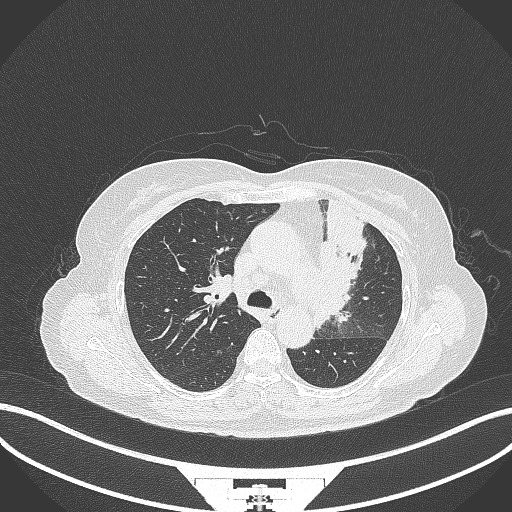
Chest CT, one axial slice; position 224 of 382 along the scan axis; lung window (W 1500 / L -600 HU); 512 × 512 image matrix. Patient: female, 64 years. From the clinical record (not read from this slice): clinical TNM (as recorded): T2a N2 M0.
Annotated regions visible in this slice (bounding box drawn by a radiologist):
- lung tumour (recorded histology: adenocarcinoma): bounding box [x1, y1, x2, y2] px = [310, 196, 372, 329]